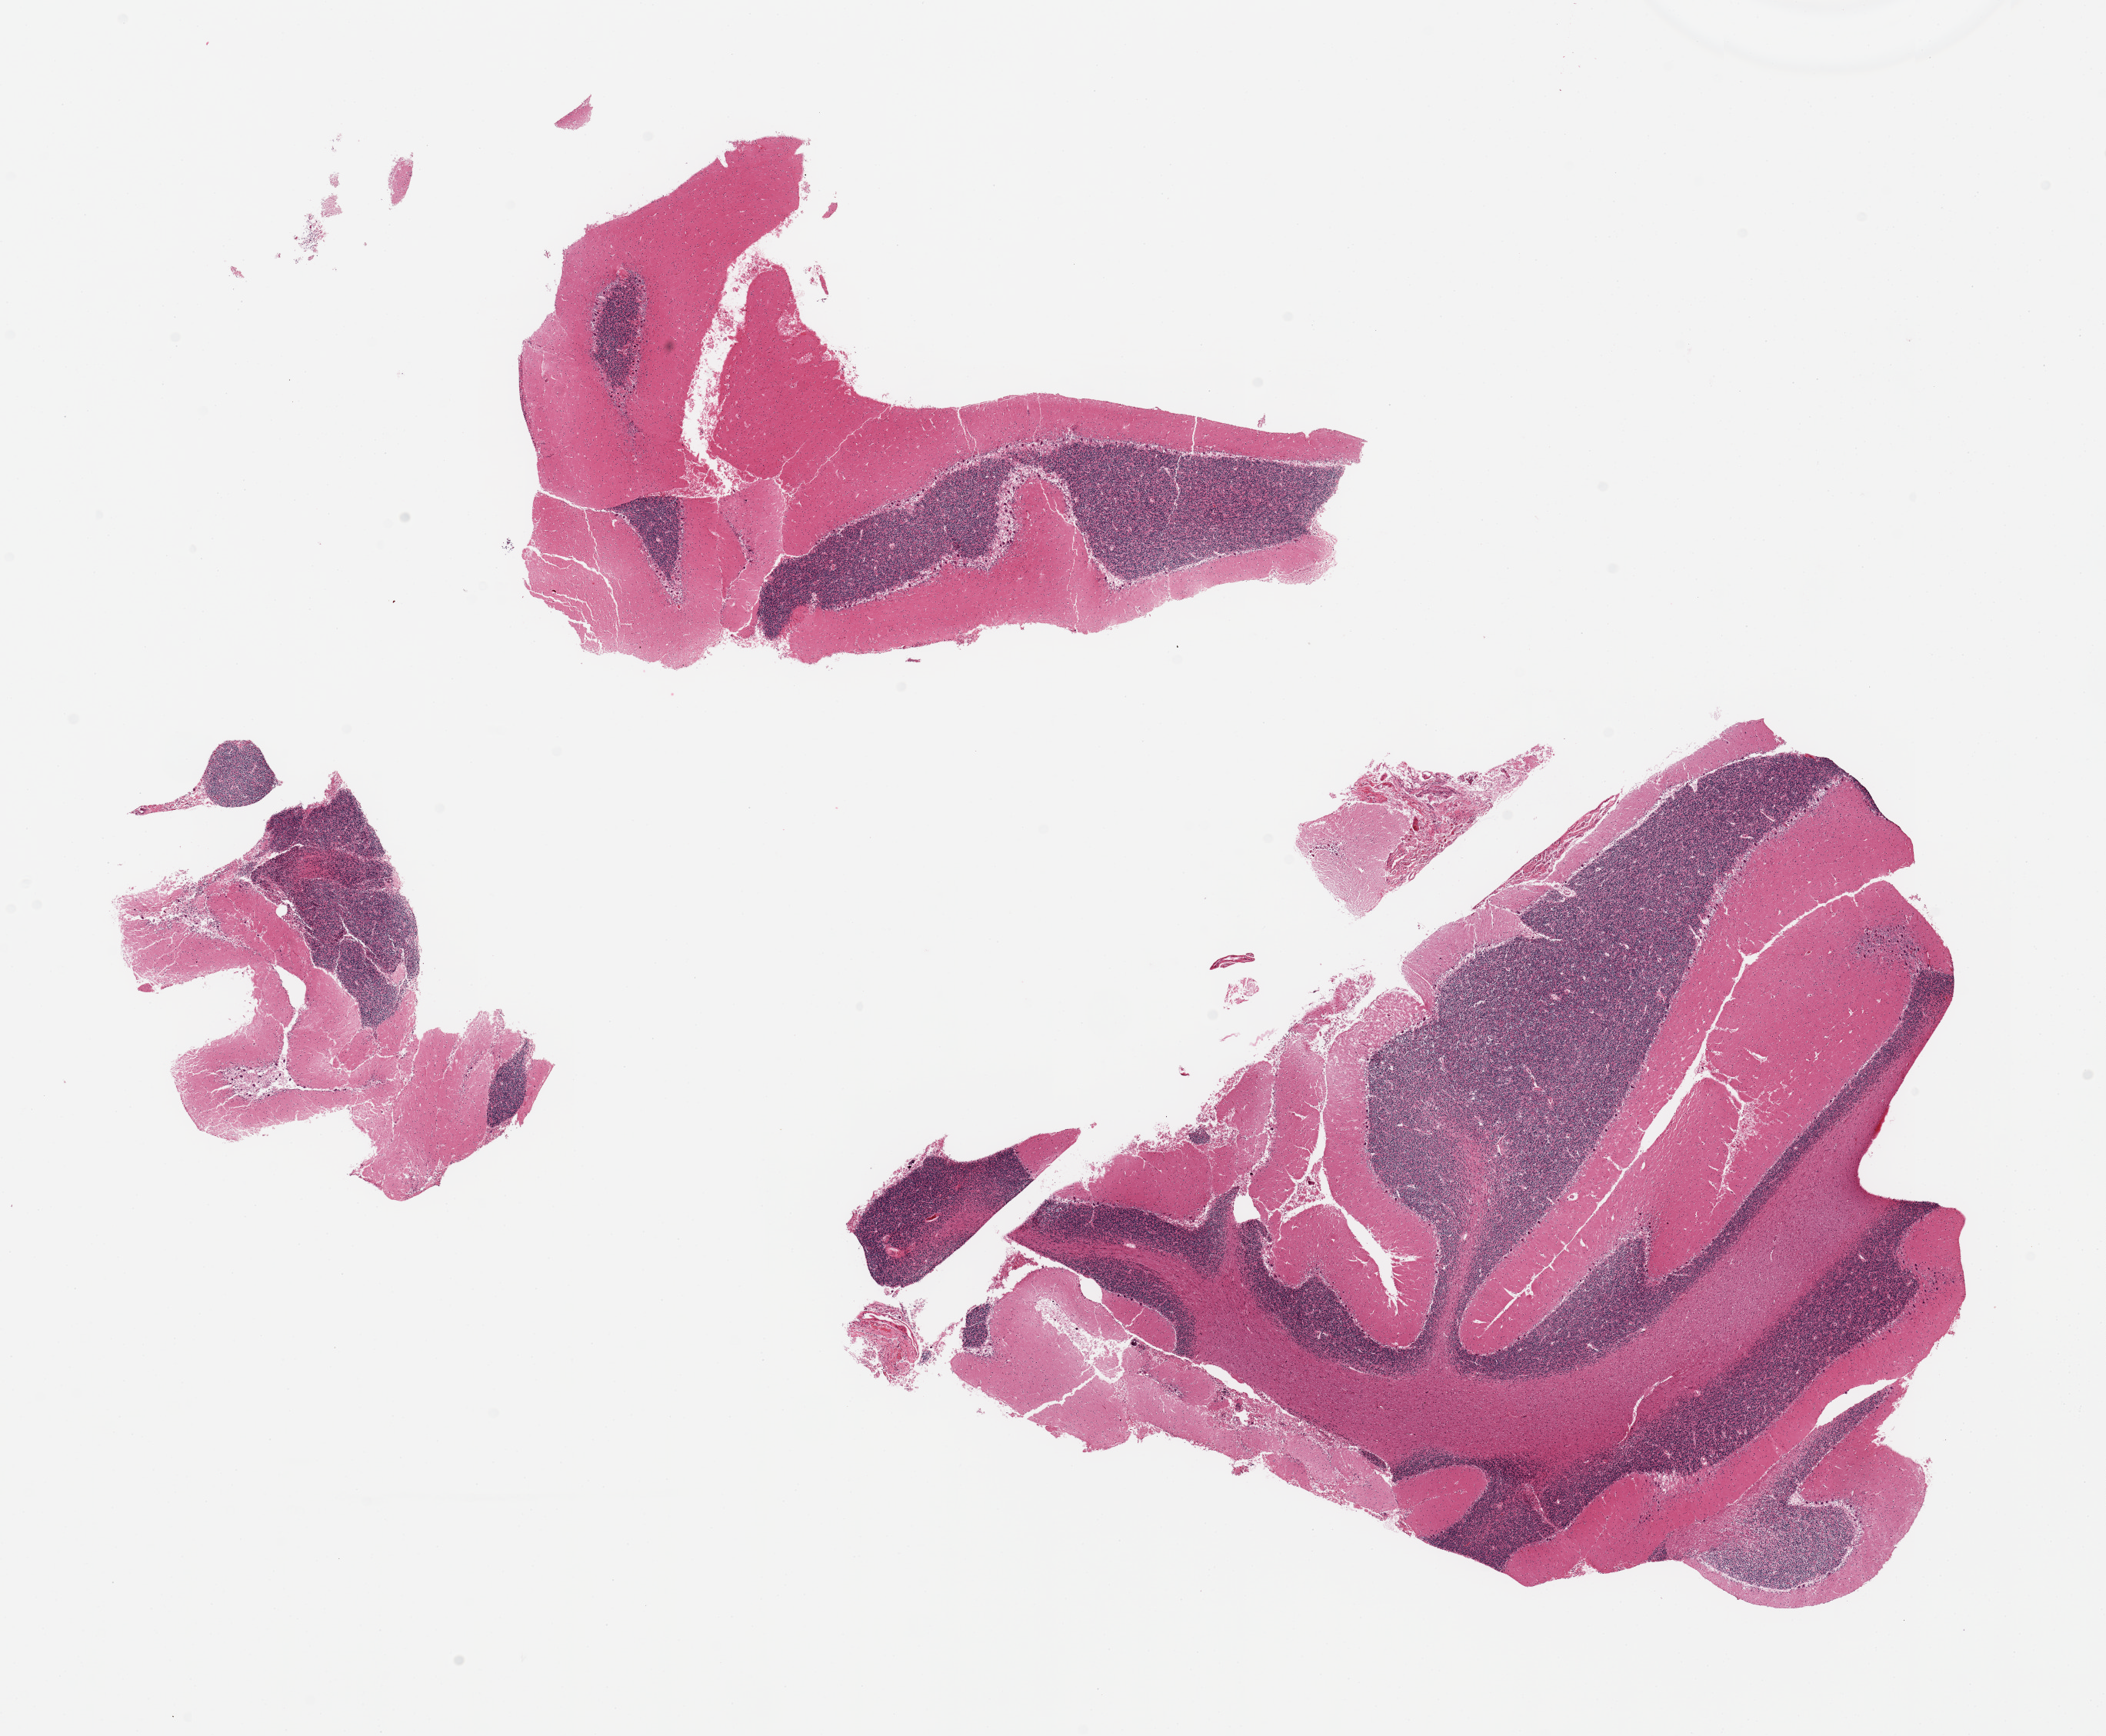
Whole-slide image, H&E stain, brightfield — shown as a low-resolution overview of the whole scanned area (about 21.7 x 17.9 mm, slide scanned at 20x); PAXgene-fixed, paraffin-embedded tissue; sampled site (target tissue): cerebellum; donor tissue sample. Donor sex: male.
• pathologist's review note for this sample: 2 pieces, fragmented. No abnormalities